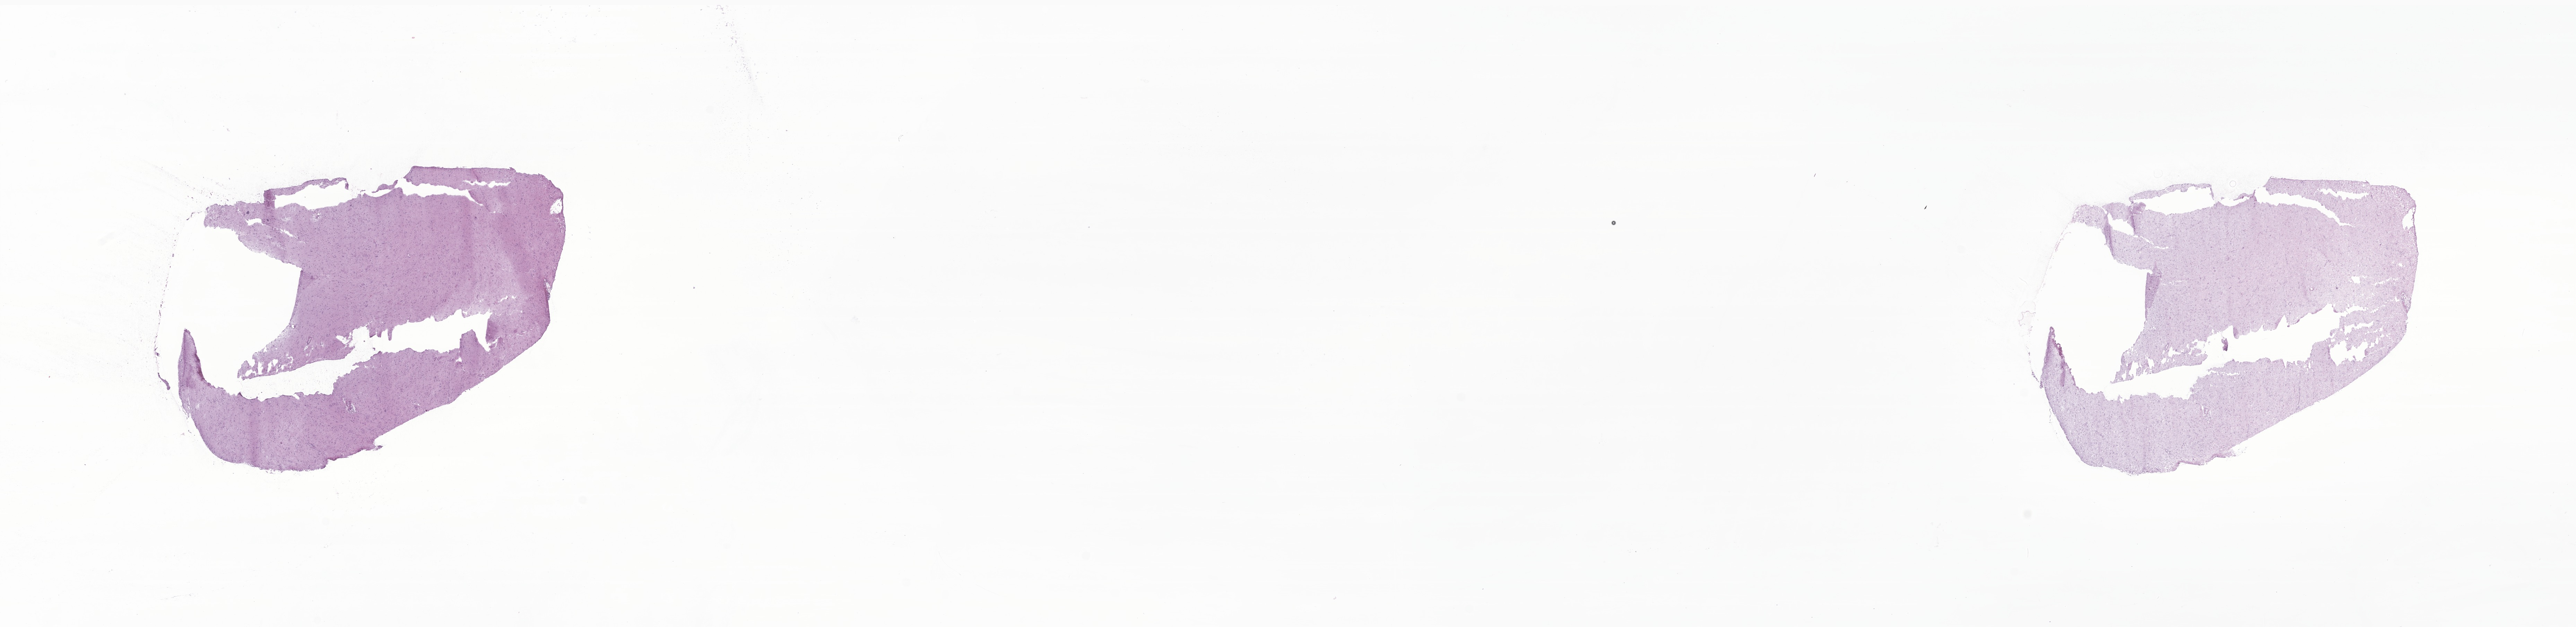
H&E whole-slide image of tumor tissue from the brain, whole scanned area (about 31.3 x 7.6 mm) shown as a low-resolution overview. Cryosection (OCT / tissue freezing medium). Patient: male, age 35 months.
Recorded diagnosis: Glioma, malignant.